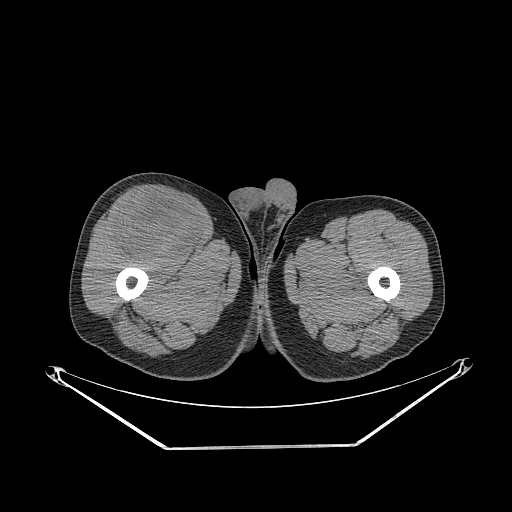
CT of an extremity soft-tissue mass (from a PET/CT study), one axial slice. Slice 284 of 311 in the series (ordered by position). 140 kVp. Soft-tissue window (W 400 / L 40 HU). 3.75 mm slice thickness. 512 × 512 image matrix, field of view 500 × 500 mm. Male patient. Case-level facts recorded for this patient, not image findings: histological type: pleiomorphic leiomyosarcoma; grade: intermediate; site of the primary tumour: right thigh.
Outlined on this slice (expert contour drawn on MRI and transferred to this co-registered scan by the dataset authors):
- gross tumour volume including surrounding oedema: bounding box <112,192,202,261> (left, top, right, bottom; pixels)
- gross tumour volume (mass): <112,192,202,261>